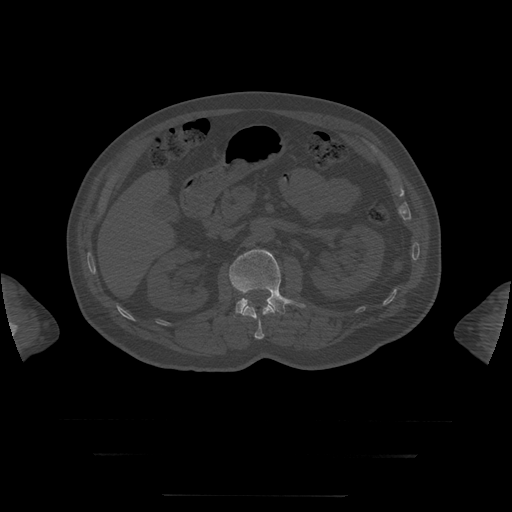
CT including the spine, one axial slice; slice 33 of 397 in the series (ordered by position); reconstruction kernel STANDARD; bone window (W 1800 / L 400 HU); 1.25 mm slice thickness; 512 × 512 image matrix. Patient age 73 years. Case-level facts recorded for this patient, not image findings: primary cancer: prostate.
Structures marked on this image (semi-automatically segmented with operator editing):
- L1 vertebra: box from (x=242, y=303) to (x=275, y=340) px